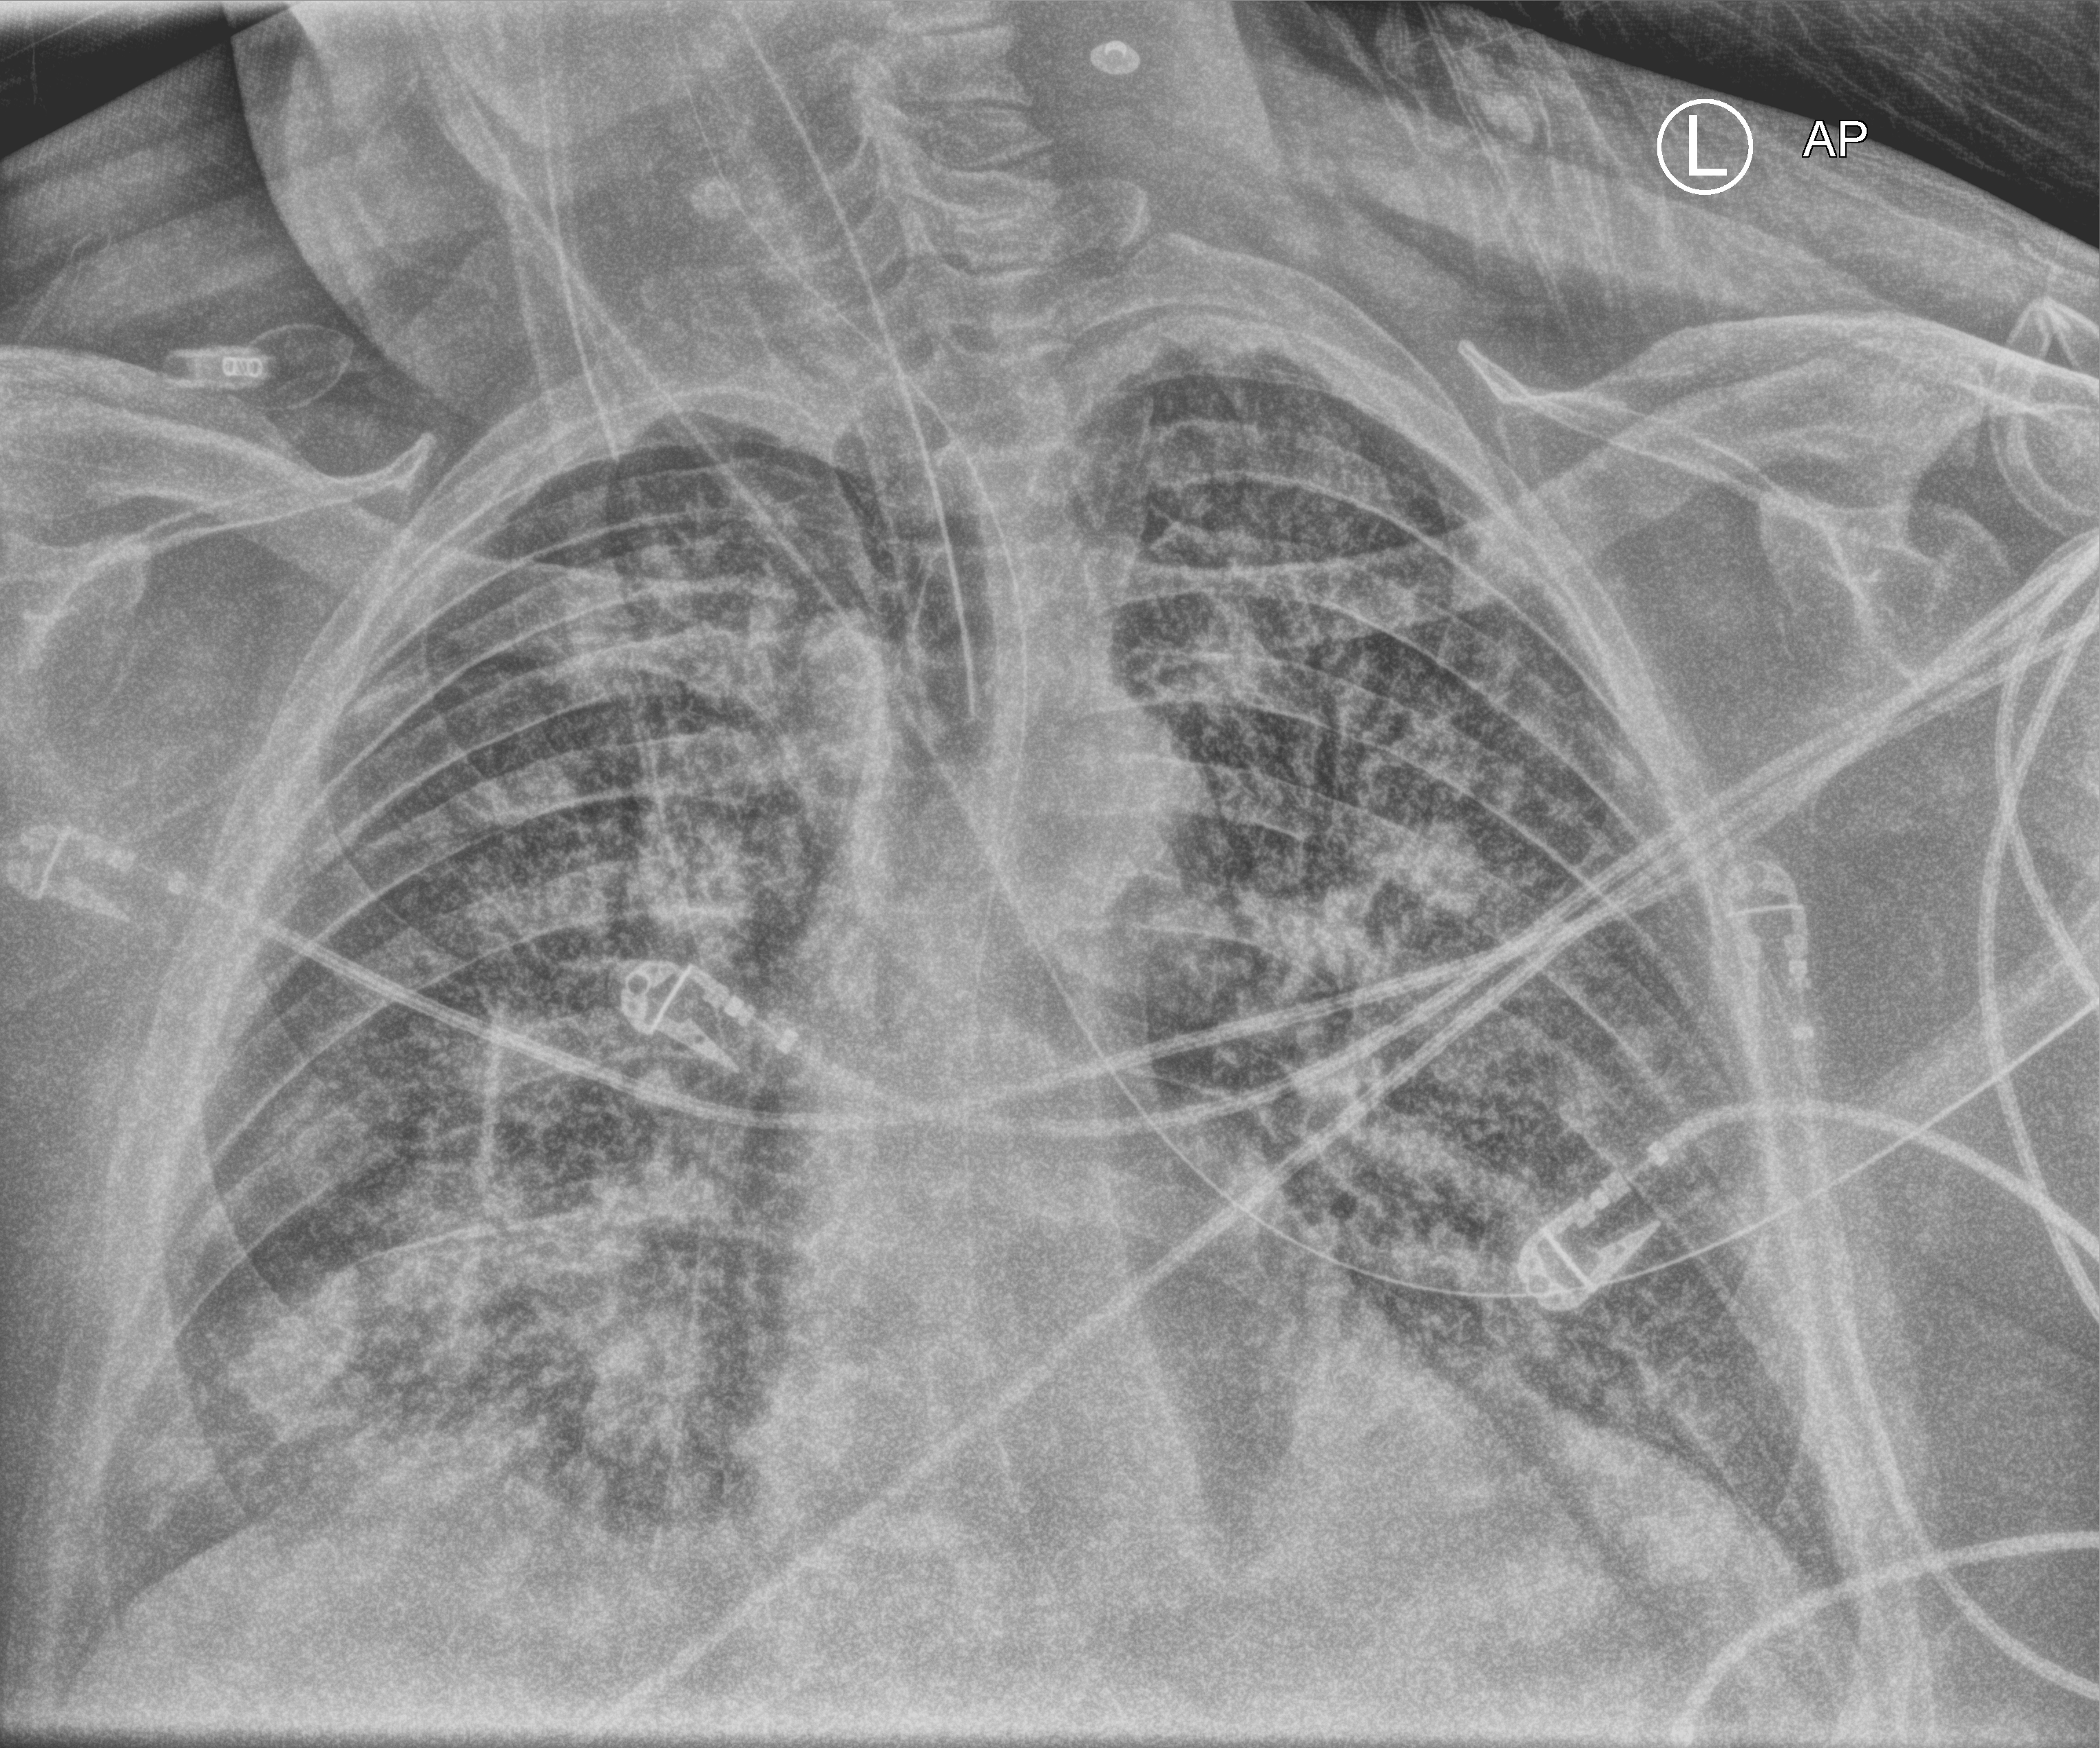
Bedside chest radiograph (computed radiography); anteroposterior (AP) projection. Patient hospitalised with COVID-19; male, aged 60–74 years.
Hospital-stay facts (about this admission, not read from this image; timing relative to this image not recorded): mechanically ventilated during this hospital stay: yes; length of hospital stay: 13 days.